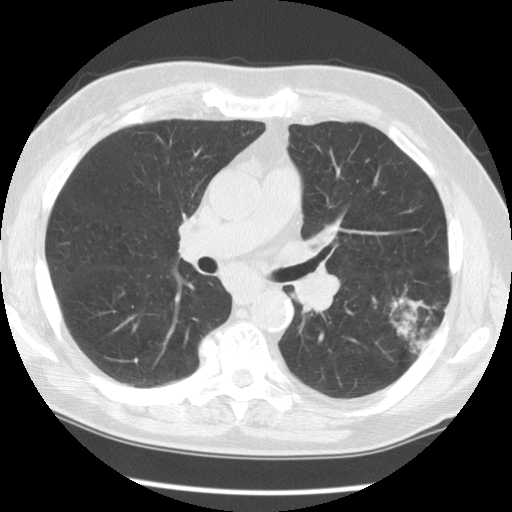
Chest CT (low-dose screening protocol), one axial image. Baseline screening round. Lung window (W 1500 / L -600 HU). Standard (soft-tissue) reconstruction kernel (STANDARD). Male, age 71 years at enrolment. Former smoker at enrolment.
• Expert reader's lesion annotation, bounding box <372,285,456,365> (left, top, right, bottom; pixels).
• The screening reader recorded 3 non-calcified nodules or masses ≥4 mm on this exam (left lower lobe, right upper lobe, right upper lobe); which of them this box marks is not recorded.